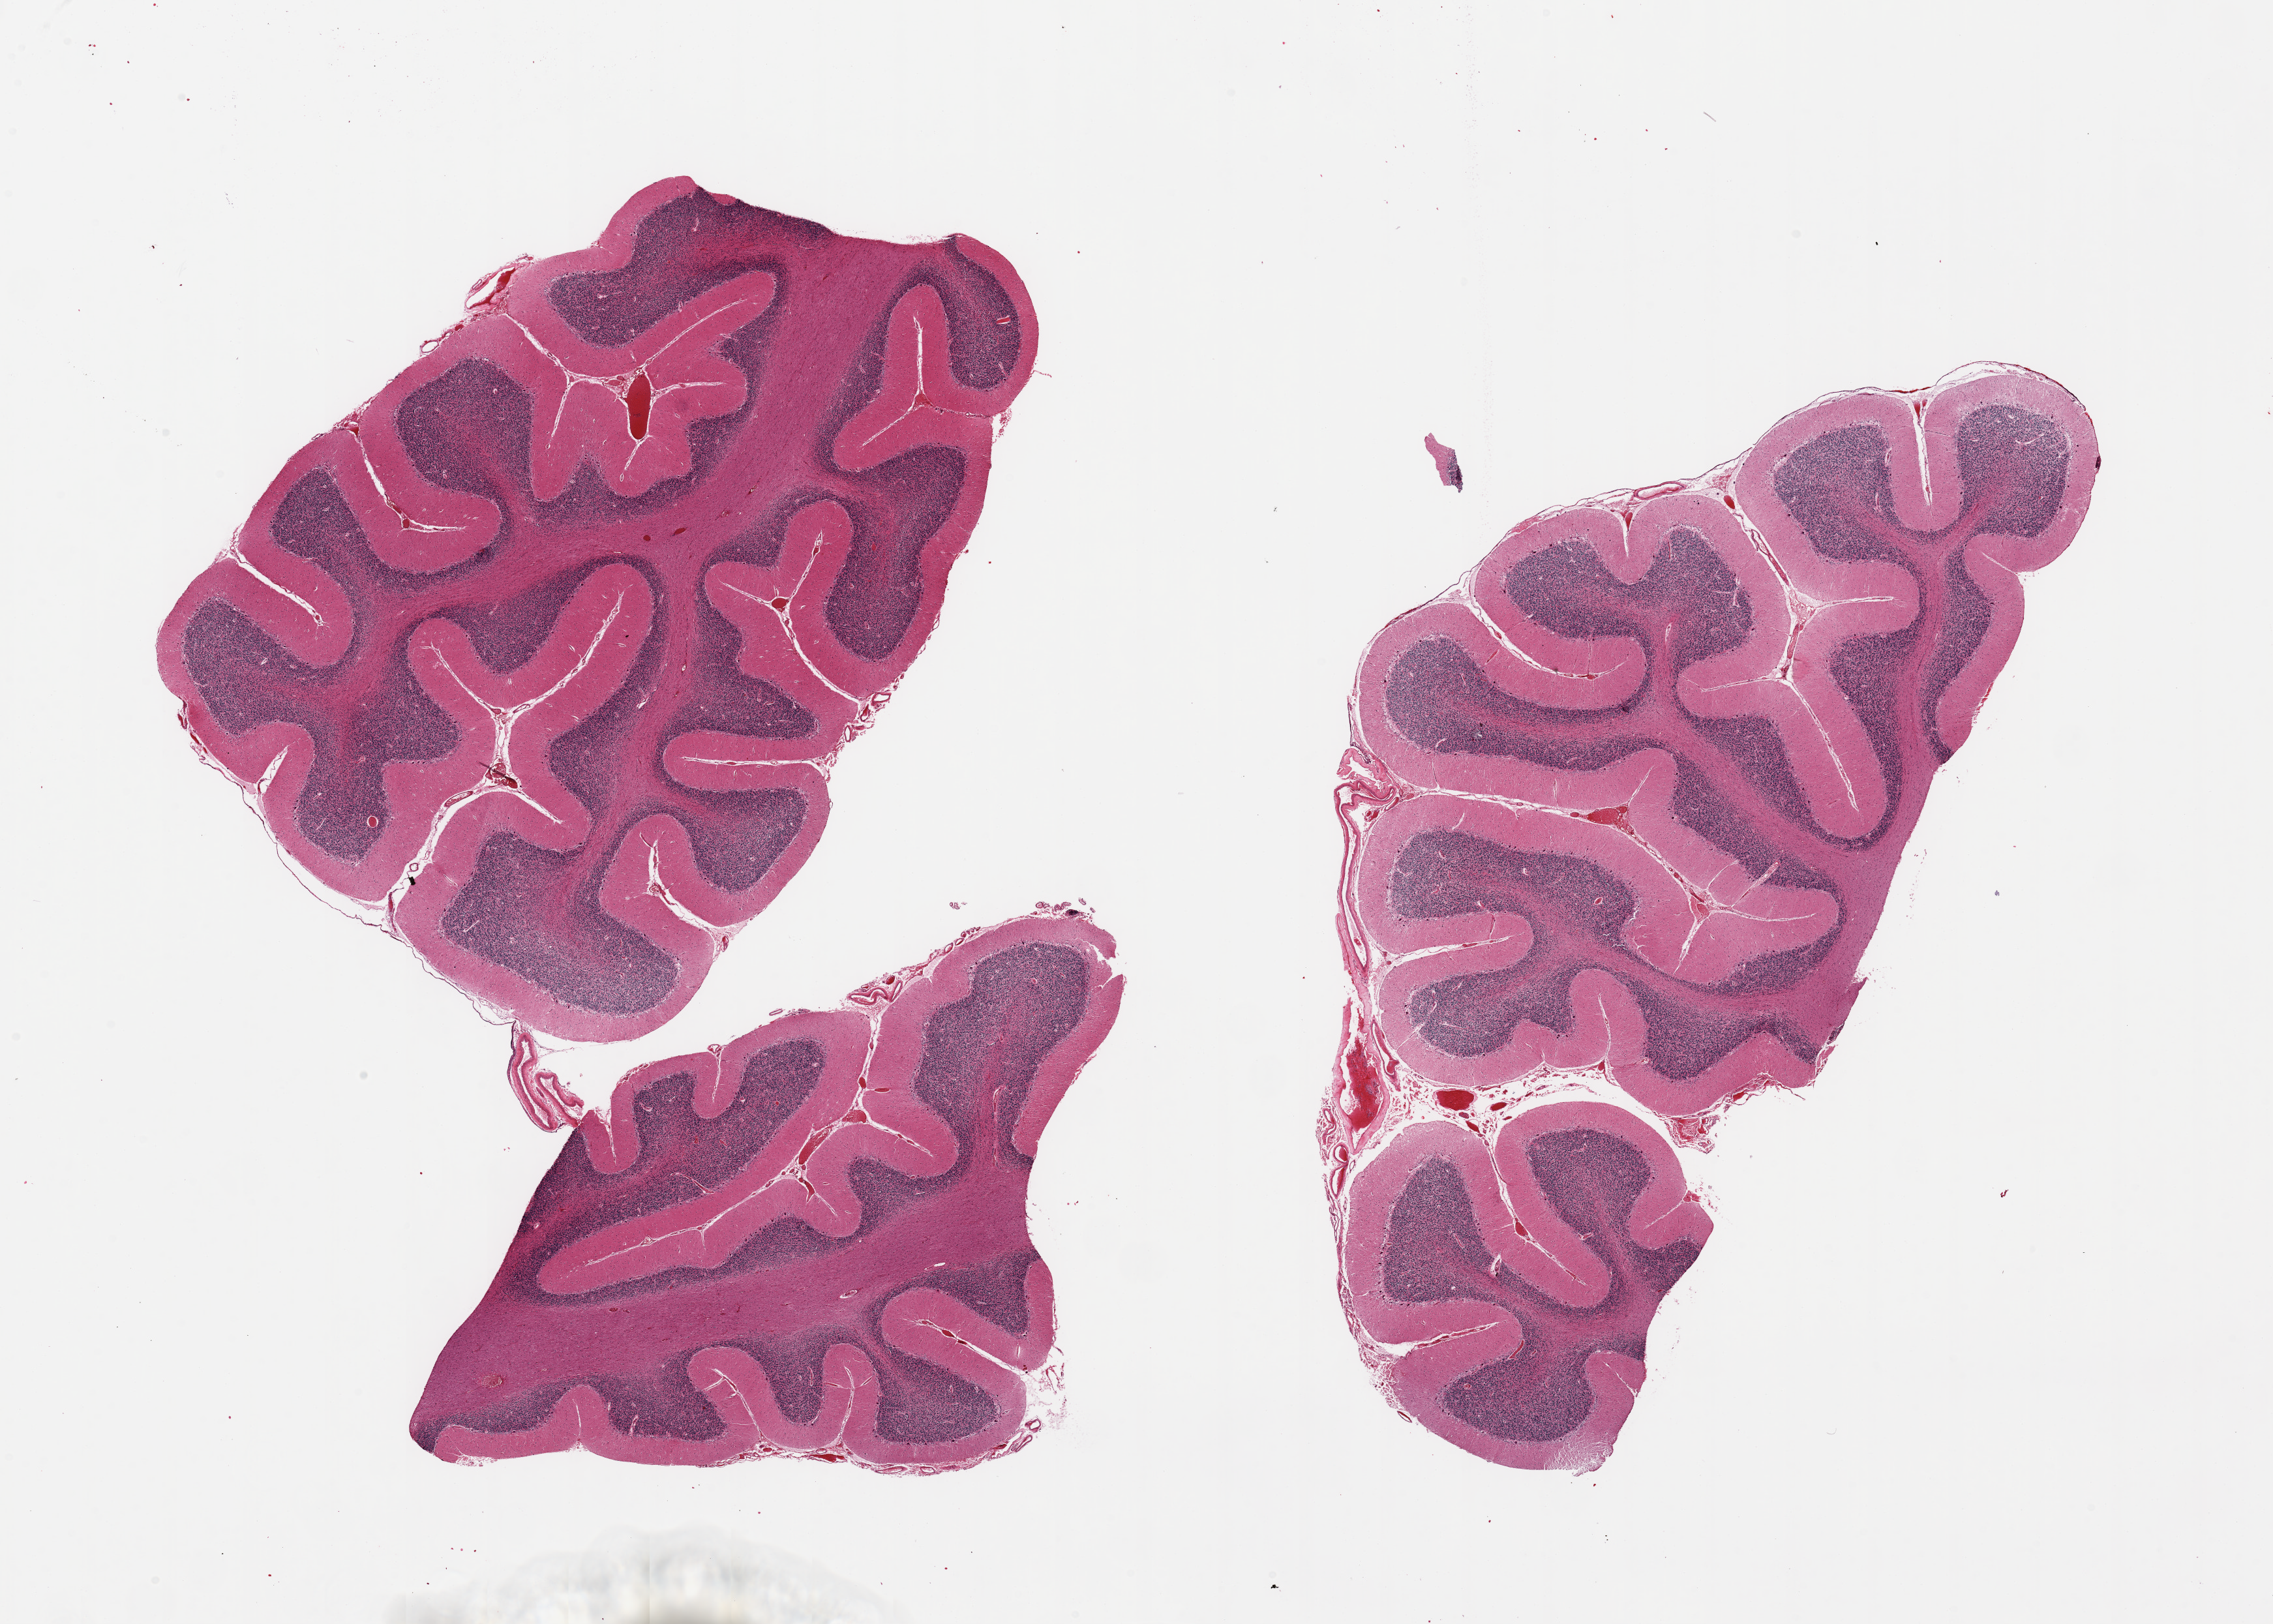
Digitized H&E-stained section, low-resolution overview of the scanned area, about 27.6 x 19.7 mm; PAXgene-fixed paraffin-embedded (PFPE) section; sampled site (target tissue): cerebellum; tissue donor sample. Donor sex: male.
• pathologist's review note for this sample: 3 pieces; residual attached meninges, Purkinje cells with some ?hypoxic change